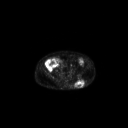
FDG PET of an extremity soft-tissue mass (from a PET/CT study), one axial slice; position 90 of 267 along the scan axis; 3.27 mm slice thickness; 128 × 128 image matrix, field of view 700 × 700 mm. Patient: male, 69 years. Case-level facts recorded for this patient, not image findings: histological type: leiomyosarcoma; grade: intermediate; site of the primary tumour: left pelvis.
Annotated regions visible in this slice (expert contour drawn on MRI and transferred to this co-registered scan by the dataset authors):
- gross tumour volume (mass): bounding box [x1, y1, x2, y2] px = [74, 78, 86, 88]